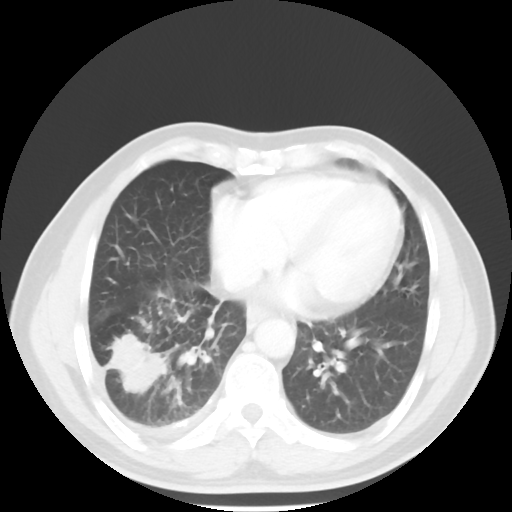
Chest CT, one axial slice; reconstruction kernel STANDARD; 120 kVp; lung window (W 1500 / L -600 HU); 512 × 512 image matrix. Patient: male, 56 years. From the clinical record (not read from this slice): clinical TNM (as recorded): T2 N3 M1.
Annotated regions visible in this slice (bounding box drawn by a radiologist):
- lung tumour (recorded histology: adenocarcinoma): bounding box <103,330,169,393> (left, top, right, bottom; pixels)